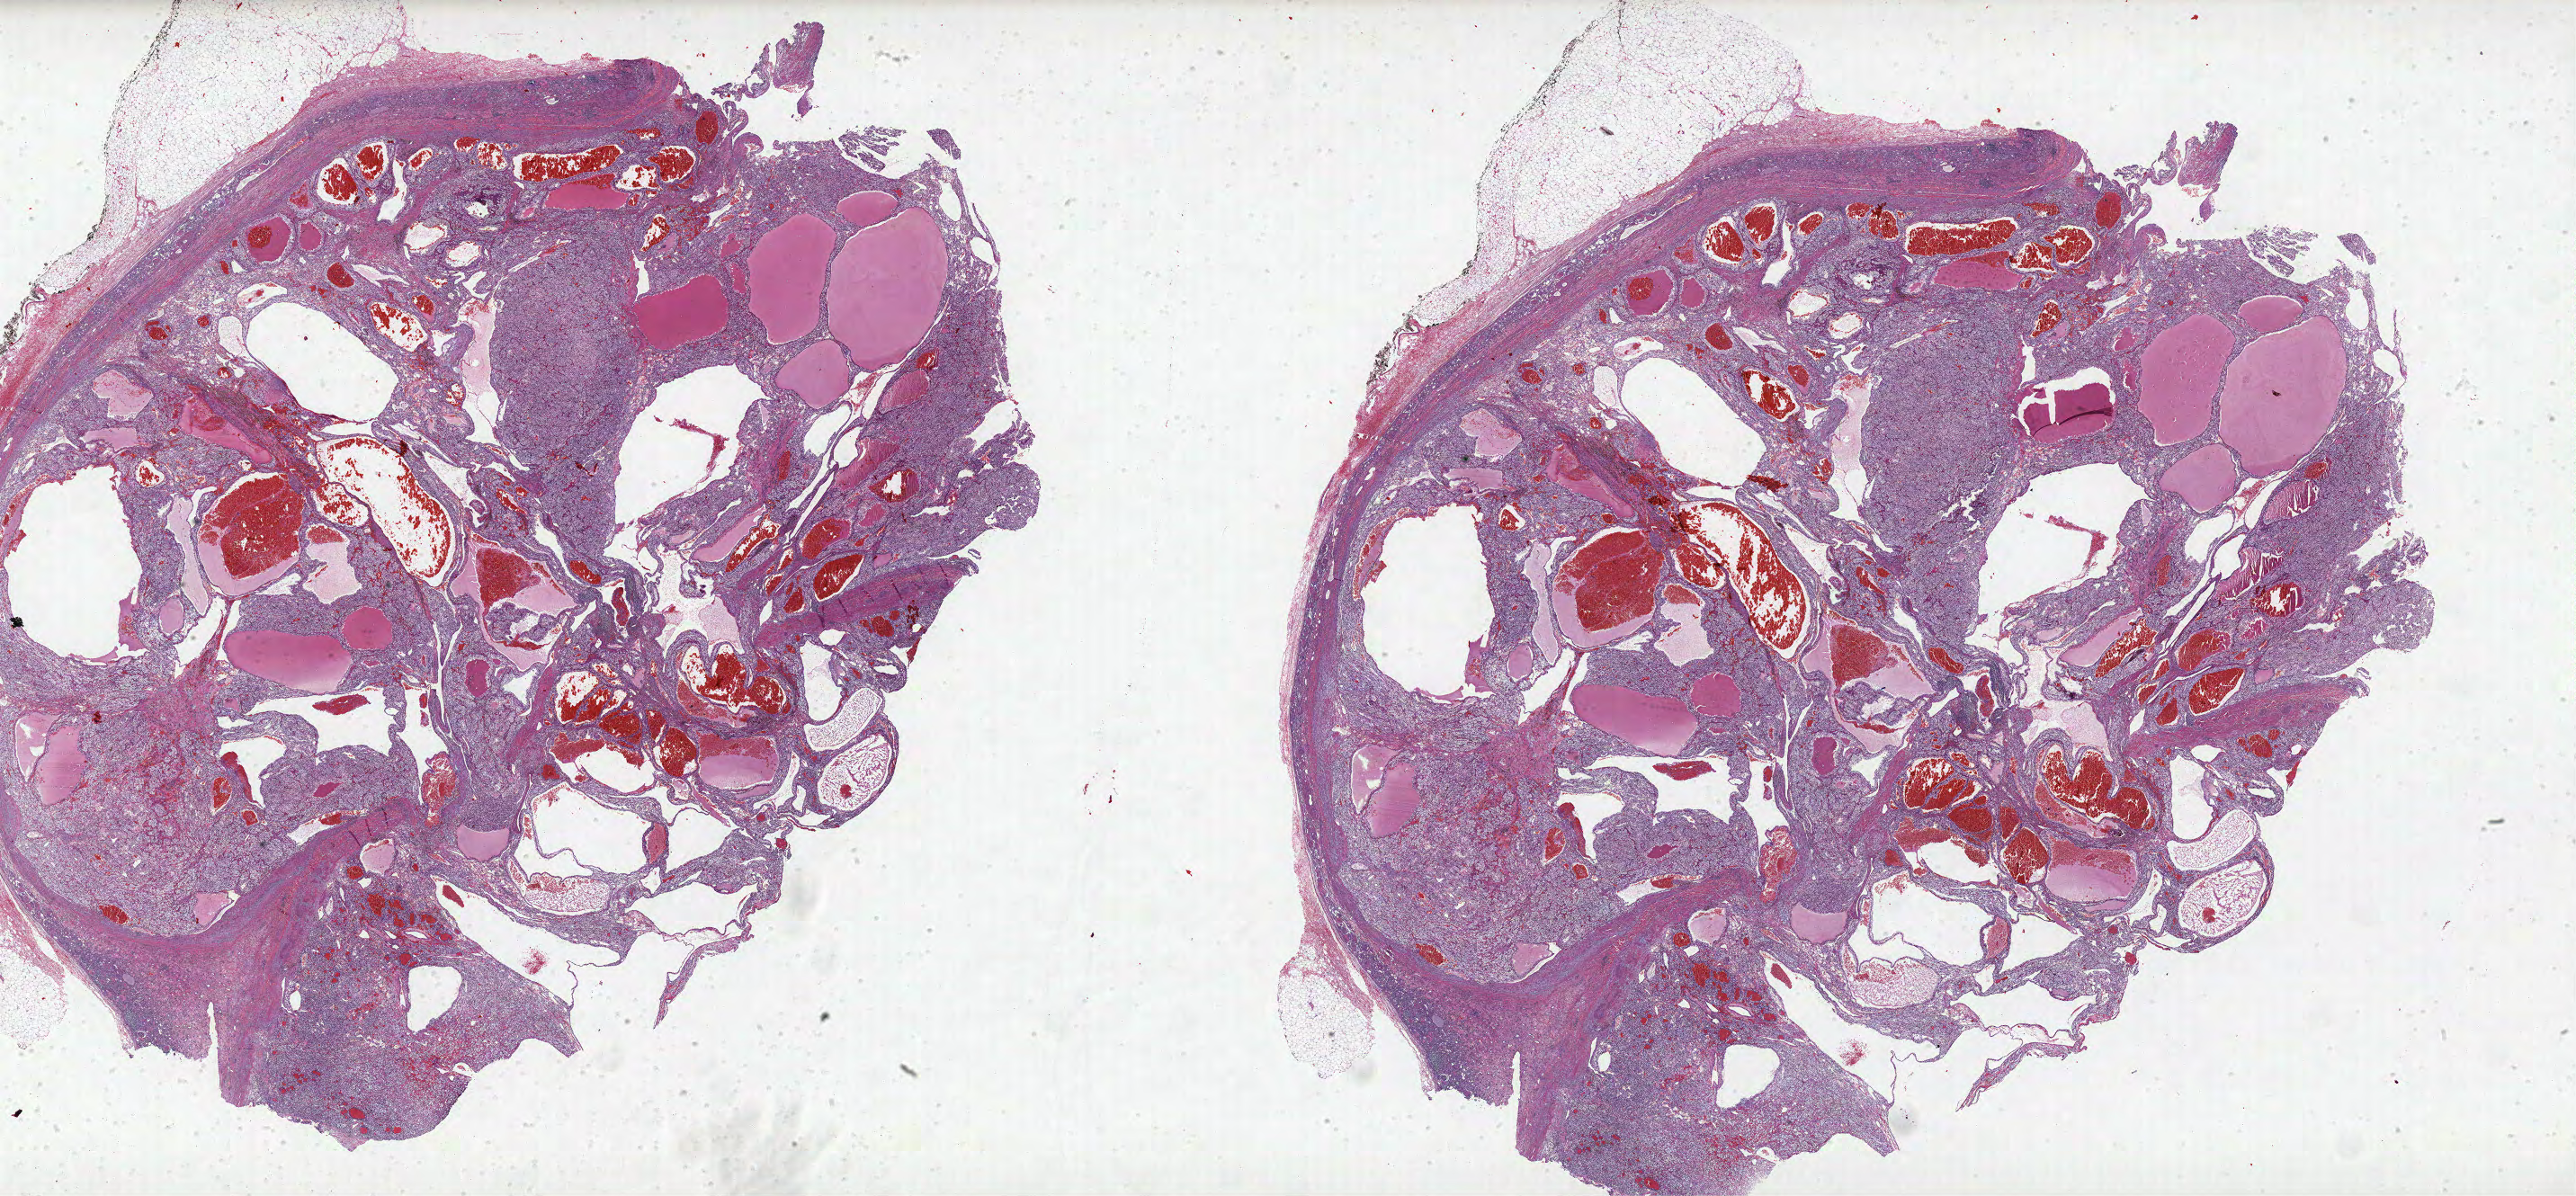
Whole-slide histology image, Hematoxylin and eosin (H&E) stained — low-resolution overview of the scanned area, about 45.8 x 21.3 mm (acquisition: 40x scan), FFPE section, primary tumour sample from the kidney. Patient: male, age at initial diagnosis 68 years.
Histologic diagnosis: Clear cell adenocarcinoma, NOS.